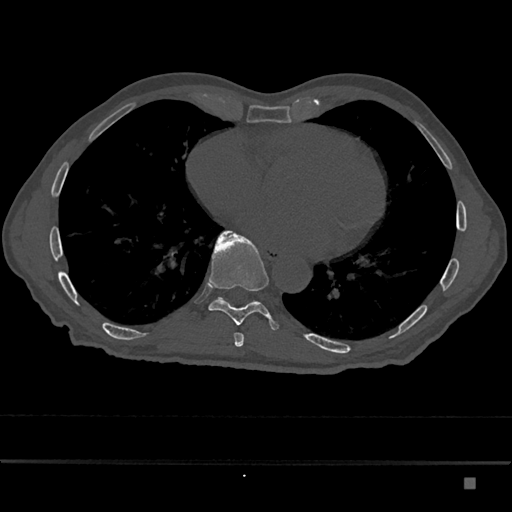
CT including the spine, one axial slice. Slice 797 of 797 in the series (ordered by position). Reconstruction kernel Br40s/3. 120 kVp. Bone window (W 1800 / L 400 HU). 512 × 512 image matrix, field of view 390 × 390 mm. Patient: male, 72 years. From the clinical record (not read from this slice): primary cancer: prostate.
Annotated regions visible in this slice (semi-automatically segmented with operator editing):
- T10 vertebra: bounding box <216,297,259,303> (left, top, right, bottom; pixels)
- T9 vertebra: <209,231,278,330>